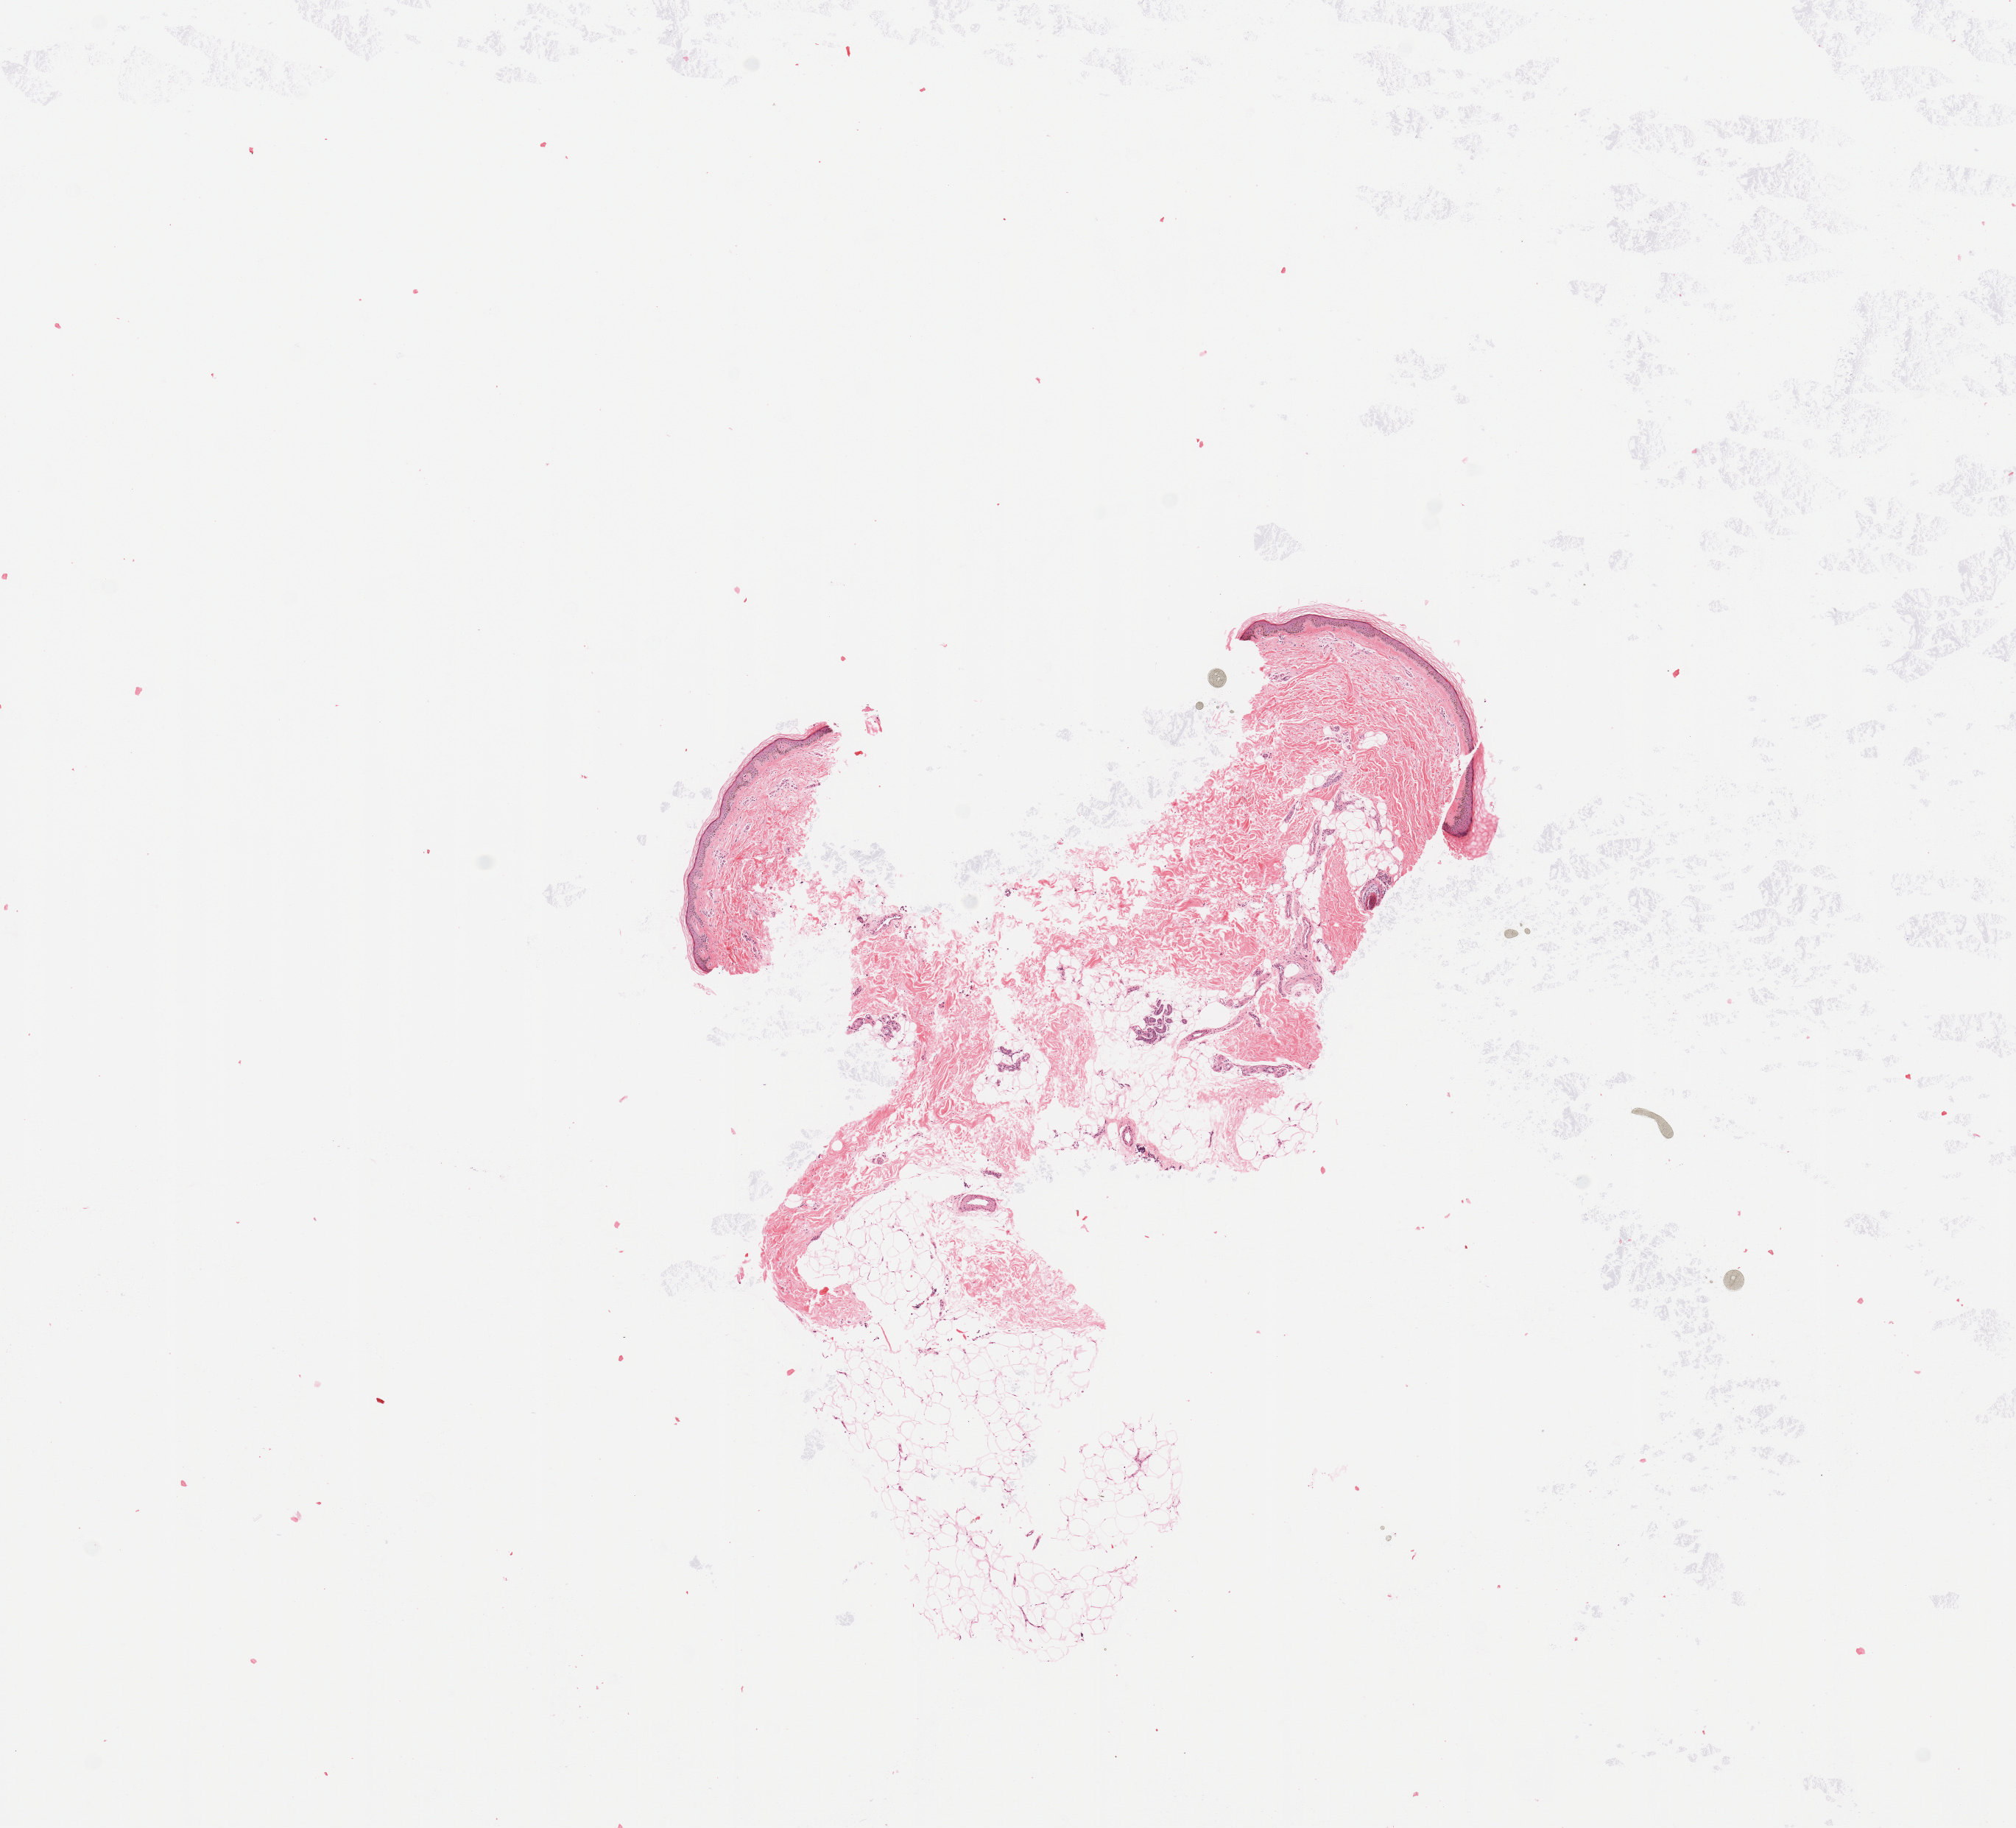
Whole-slide histology image, H&E-stained, a low-resolution overview of the entire scanned area, about 10.8 x 9.8 mm (slide scanned at 20x); normal (non-tumour) tissue (melanoma cohort); sampled site not recorded. Female, 64 y/o.
This section: normal (non-tumour) tissue from the same patient. Patient diagnosis: Malignant melanoma, NOS.